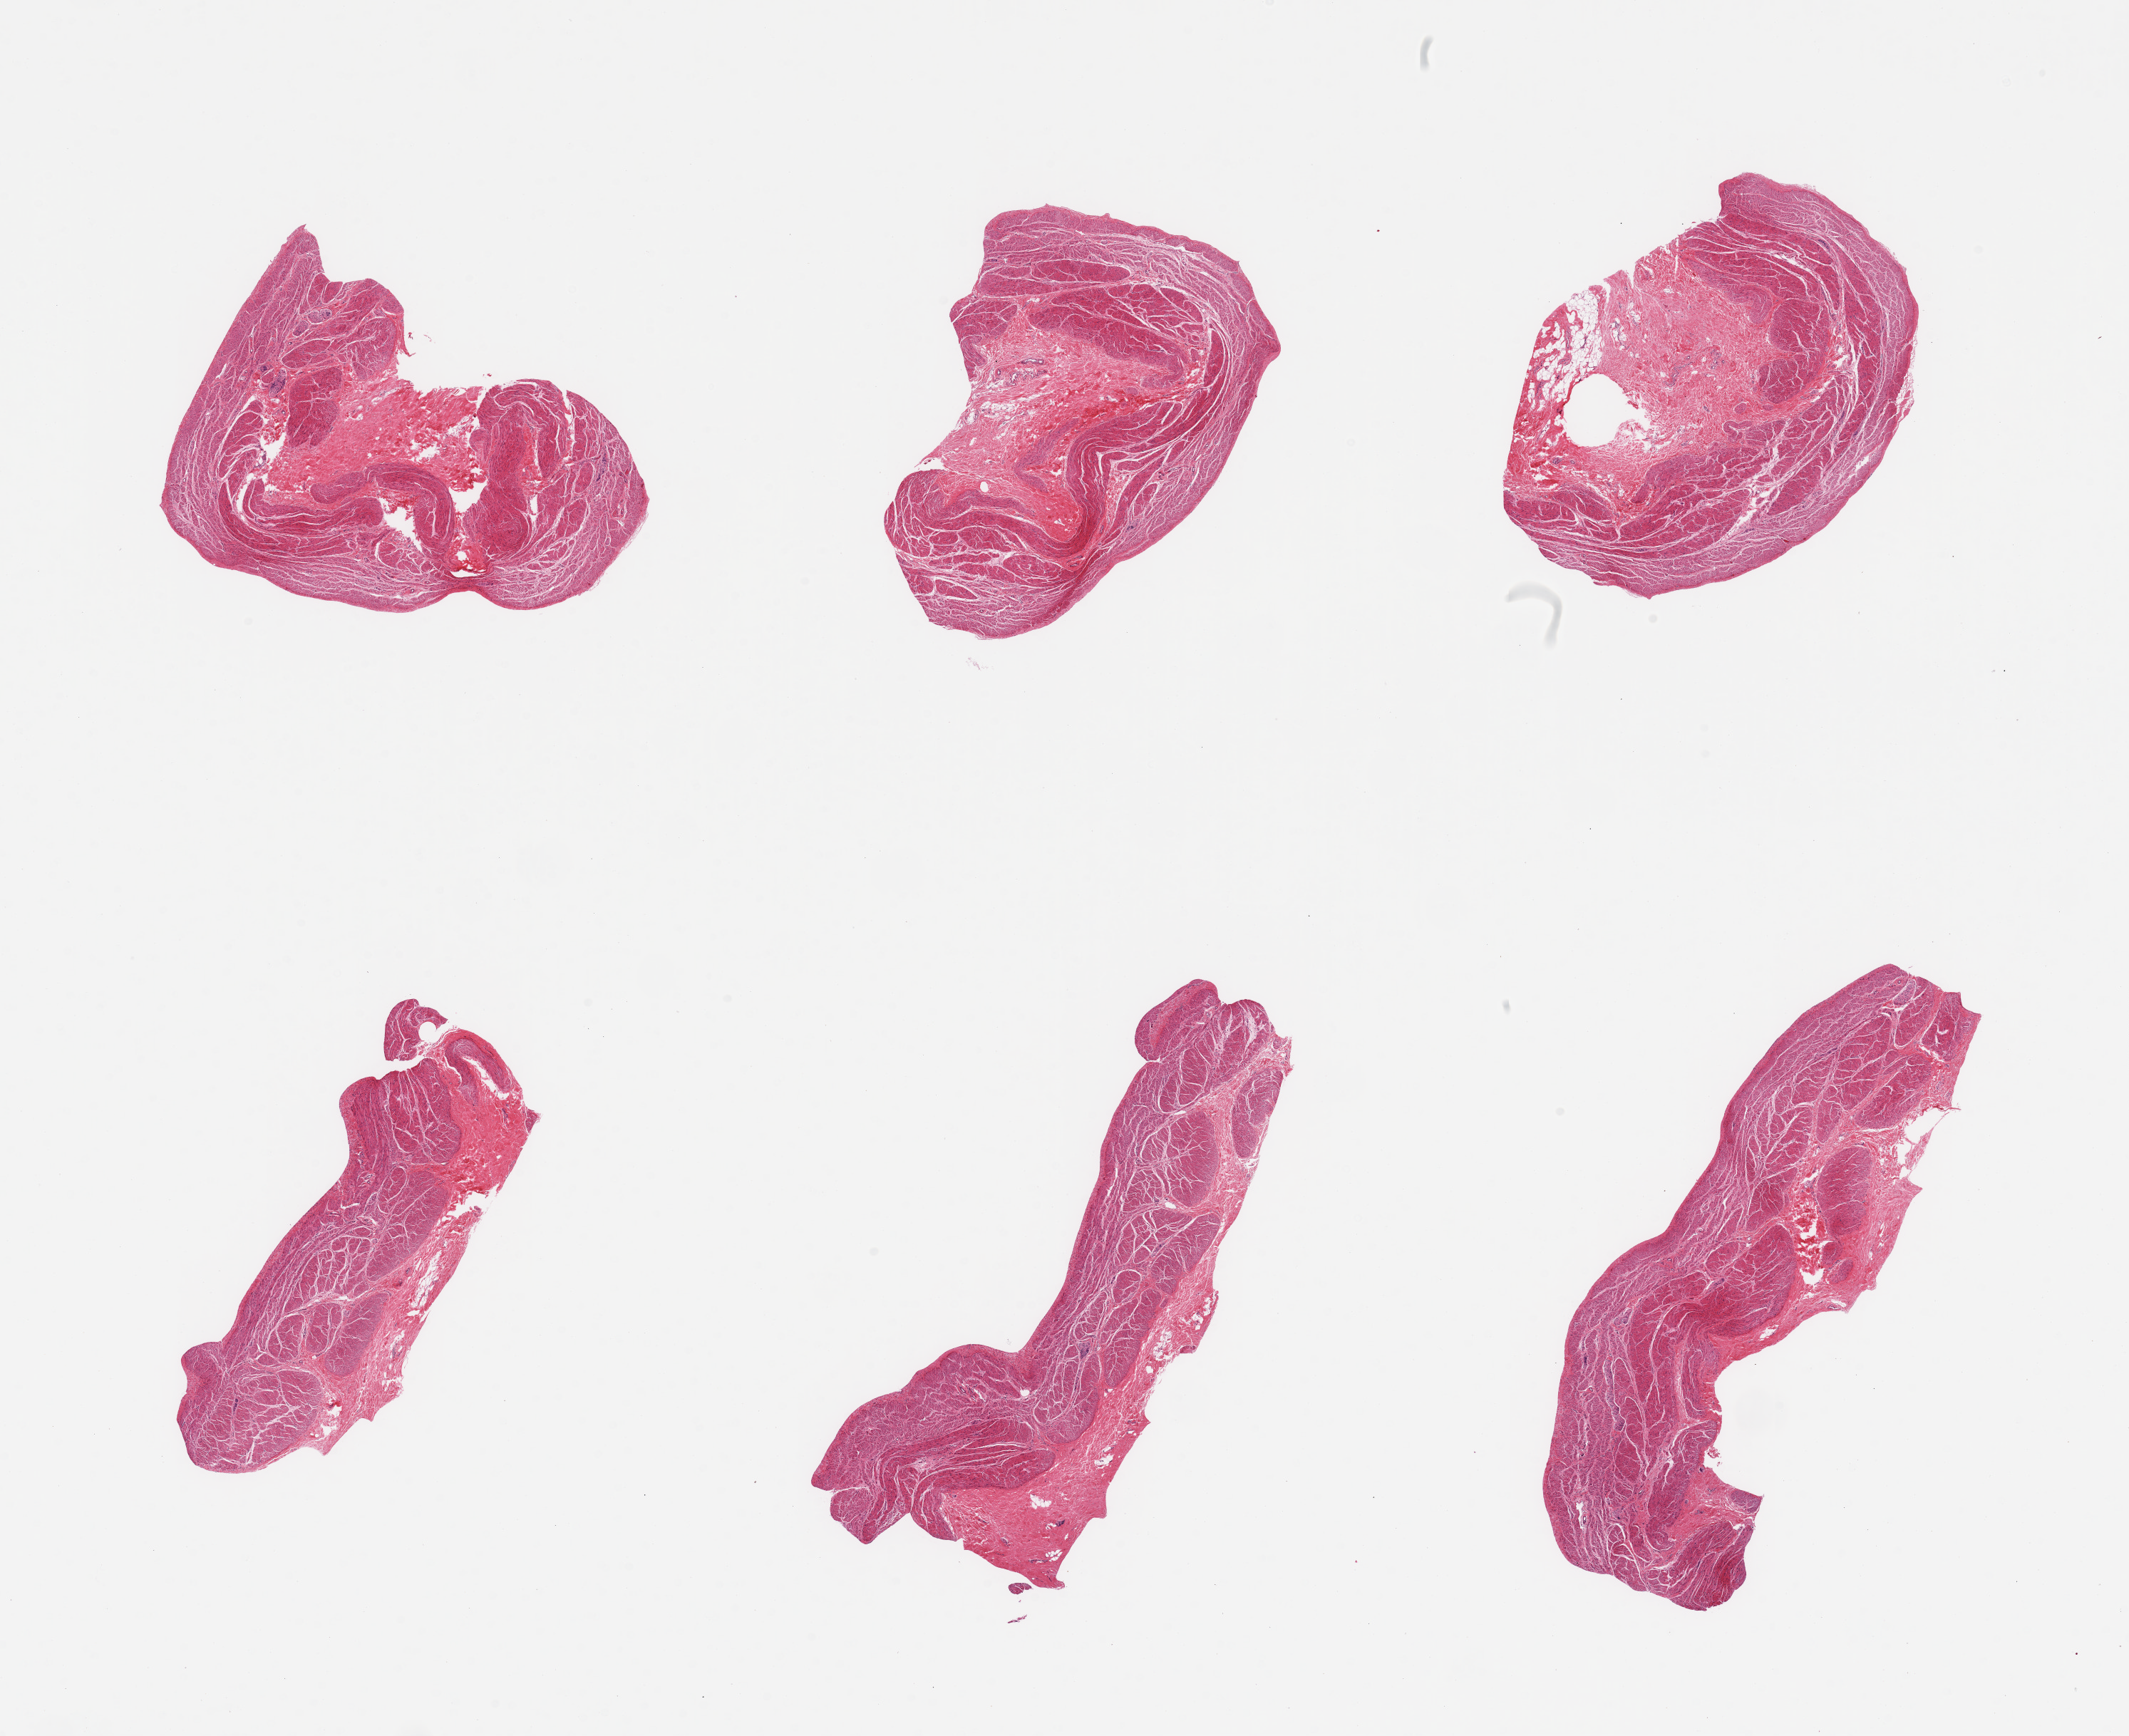
Whole-slide image, H&E stain — whole scanned area (about 23.6 x 19.3 mm, from a 20x scan) shown as a low-resolution overview. PAXgene-fixed paraffin-embedded (PFPE) section. Section of stomach (target tissue). Tissue donor sample.
- review note (as recorded): 6 pieces; muscularis propria and submucosa only, no mucosa